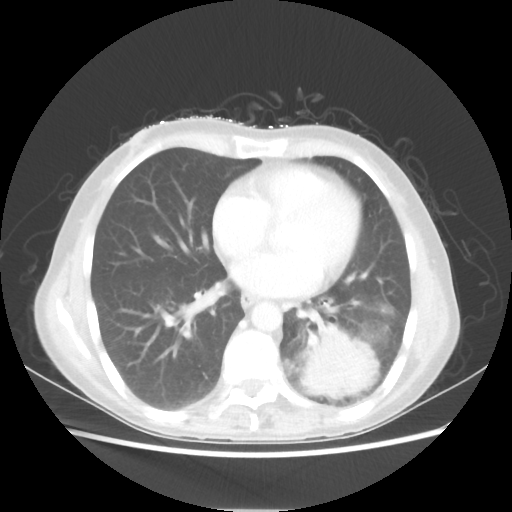
Chest CT, one axial slice; position 24 of 56 along the scan axis; lung window (W 1500 / L -600 HU); 512 × 512 image matrix, field of view 360 × 360 mm. Patient: female, 53 years. From the clinical record (not read from this slice): clinical TNM (as recorded): T3 N0 M0.
Outlined on this slice (bounding box drawn by a radiologist):
- lung tumour (recorded histology: adenocarcinoma): box from (x=299, y=322) to (x=379, y=400) px